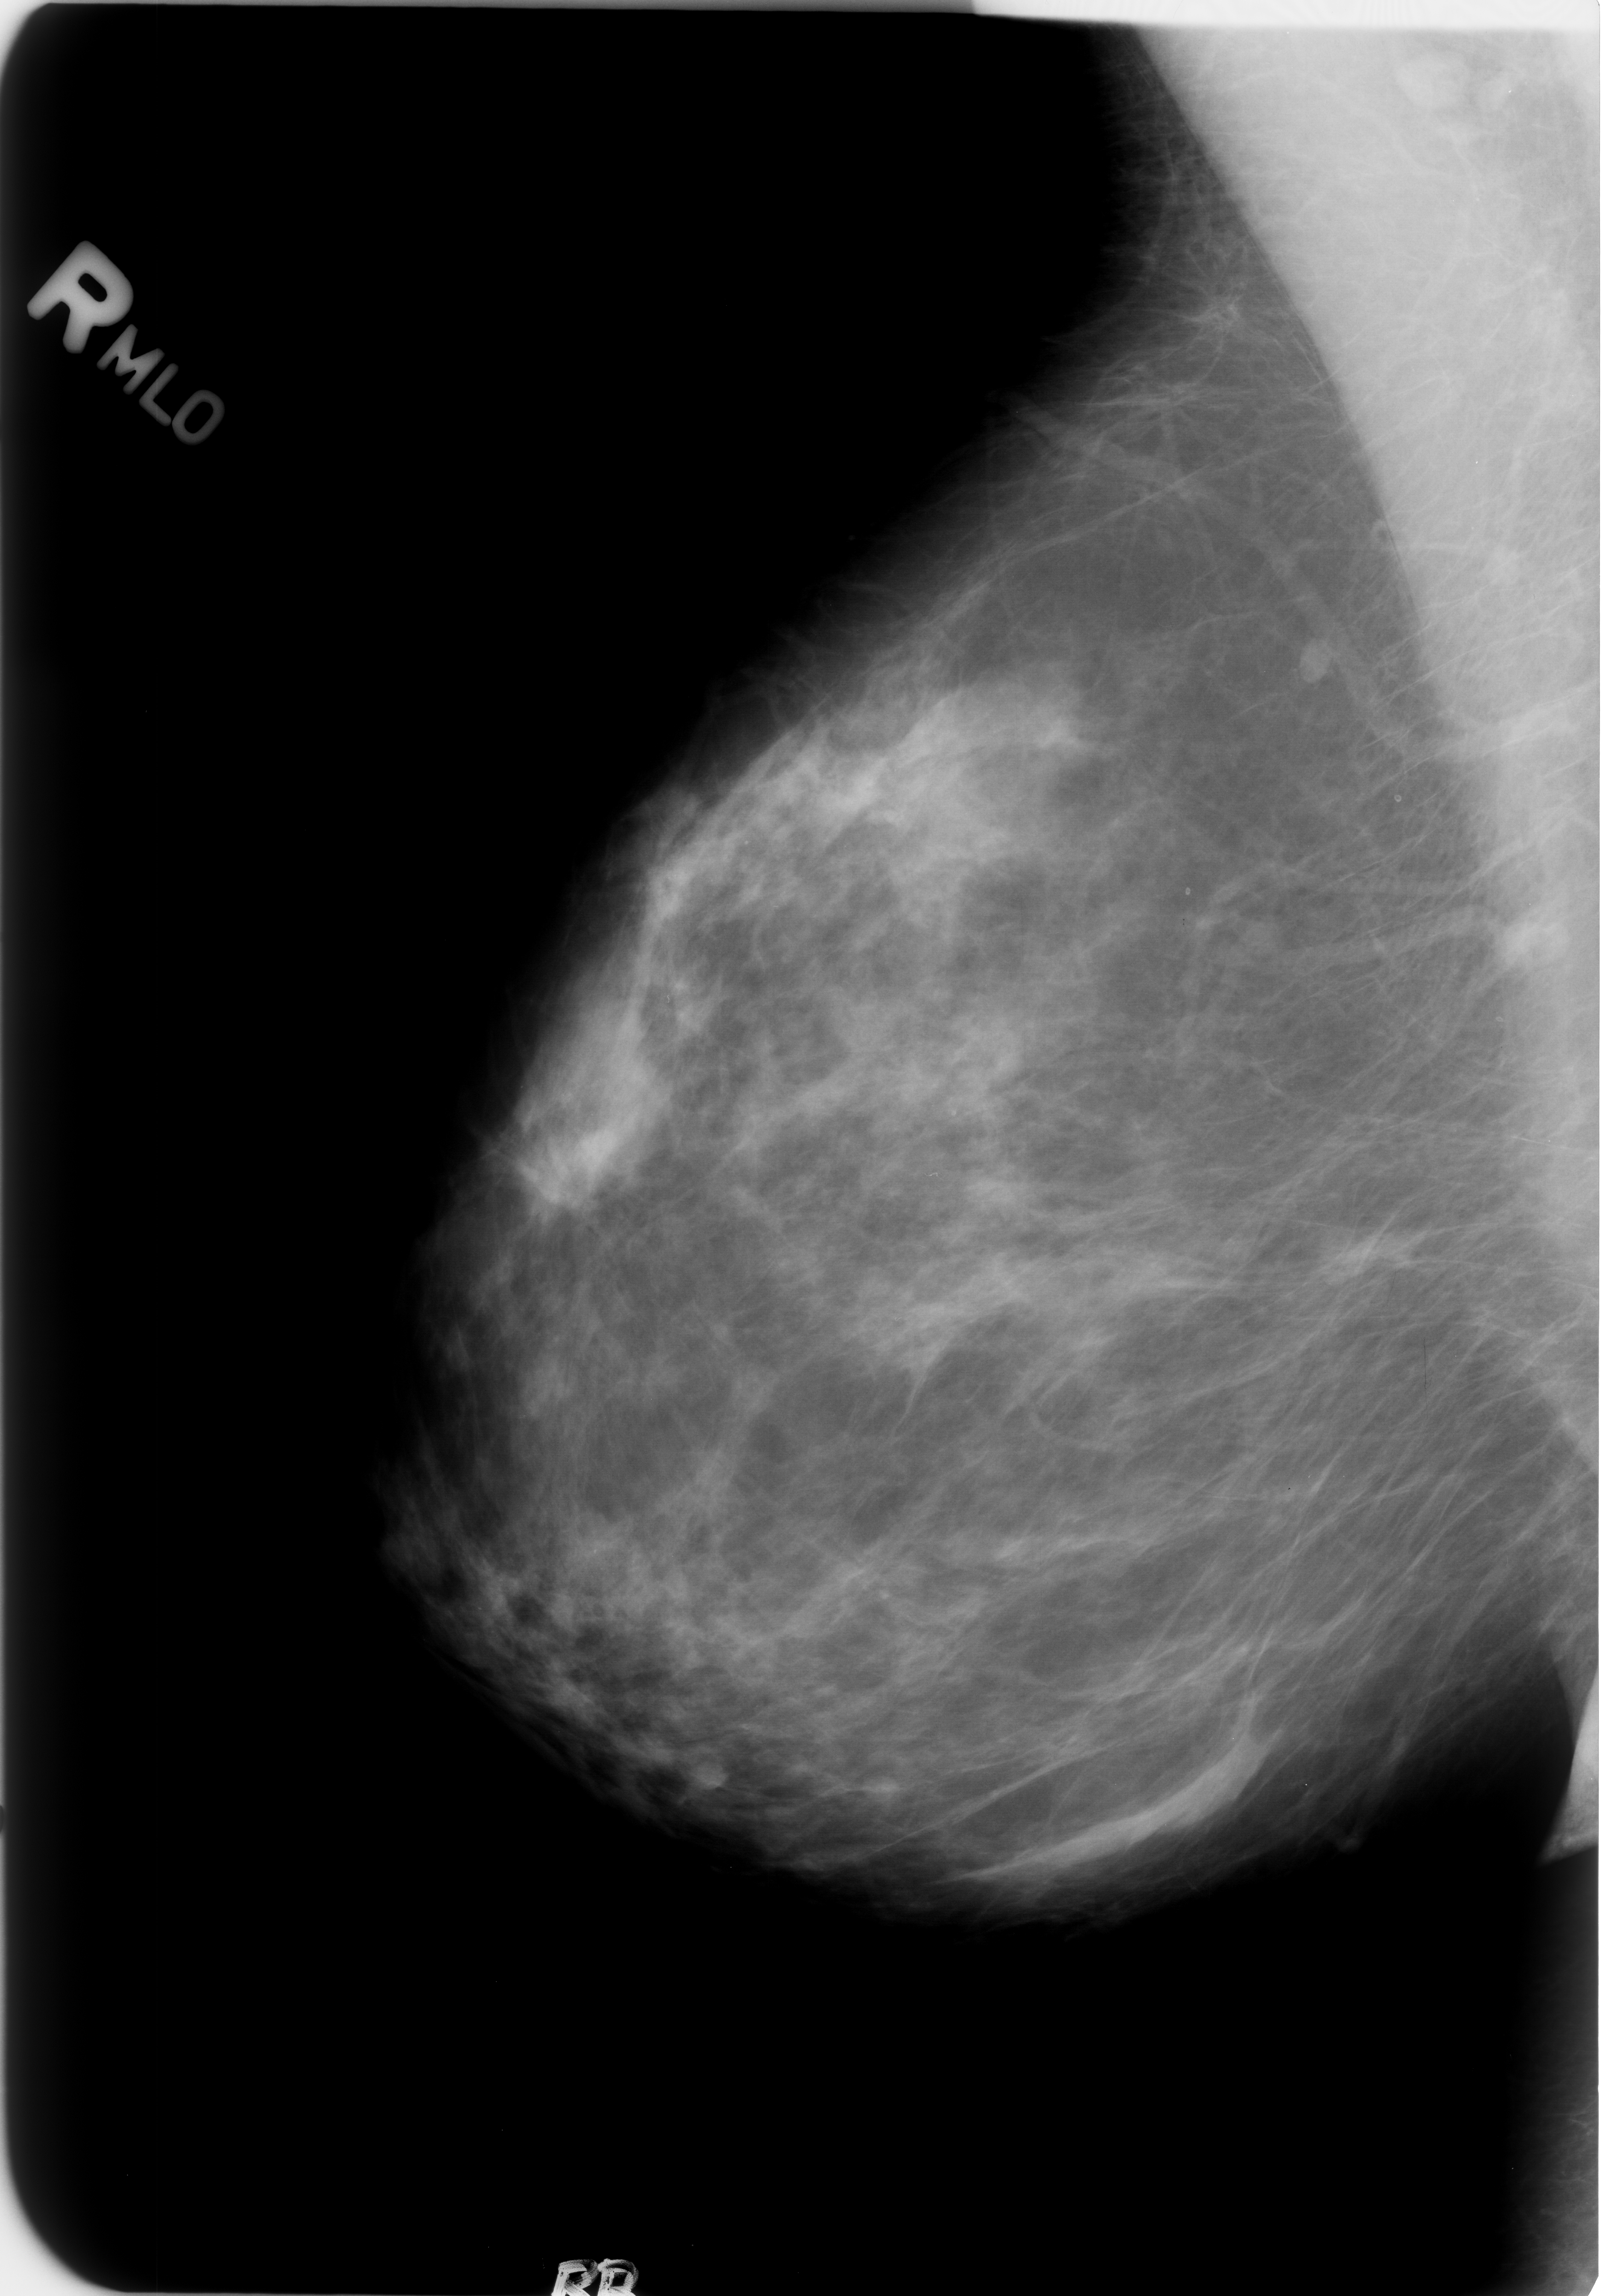
Scanned film-screen mammogram; right breast; MLO view; BI-RADS breast density category 2 (scale 1–4); 1605 × 2296 image matrix.
Marked abnormalities (boxes around the expert regions of interest):
- Finding 1 of 3: calcifications, morphology lucent center; BI-RADS assessment category 2; subtlety rating 3 on a 1 (subtle) to 5 (obvious) scale; benign; no additional work-up was recommended (outcome (as recorded, no biopsy): benign without callback): bounding box (x1, y1, x2, y2) in pixels: (1171, 878, 1201, 912)
- Finding 2 of 3: calcifications, morphology lucent center; BI-RADS assessment category 2; outcome (as recorded, no biopsy): benign without callback (not worked up further): (1382, 786, 1405, 810)
- Finding 3 of 3: calcifications, morphology lucent center; BI-RADS assessment category 2; subtlety rating 3 on a 1 (subtle) to 5 (obvious) scale; benign; no additional work-up was recommended (outcome (as recorded, no biopsy): benign without callback): (1487, 996, 1526, 1026)